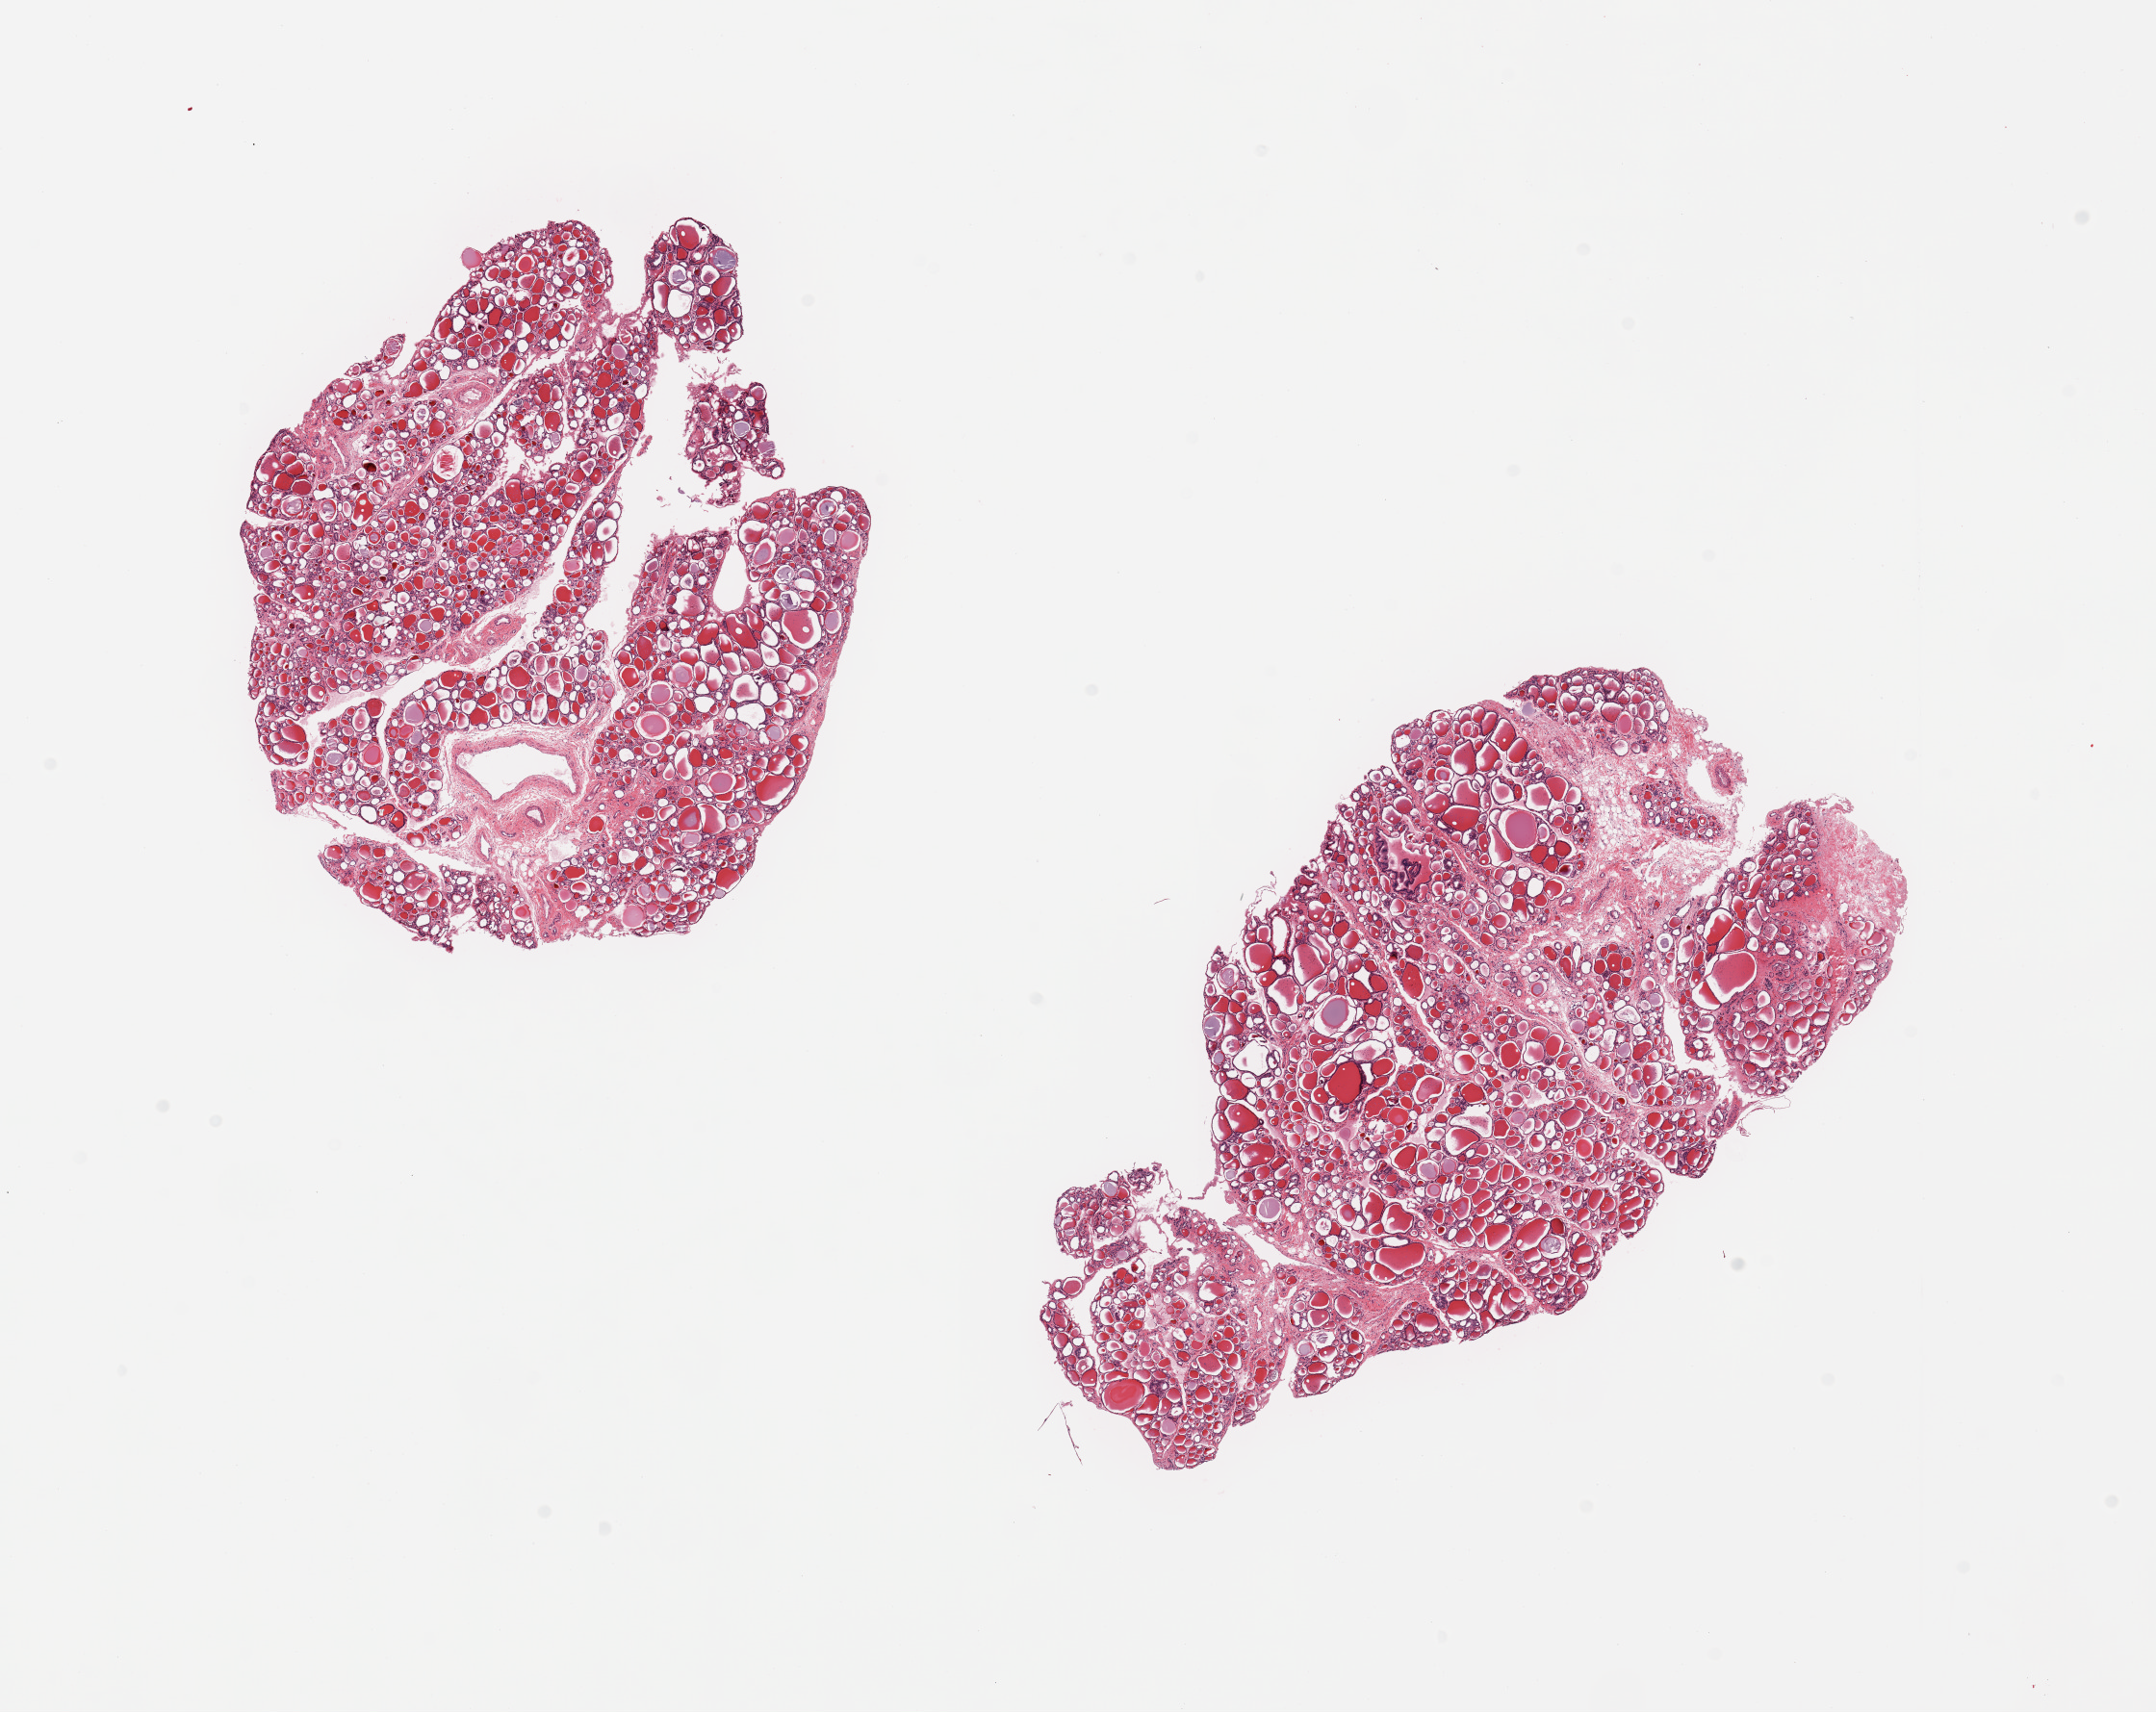
Whole-slide image, hematoxylin and eosin (H&E) stain, low-resolution overview of the scanned area, about 17.7 x 14.1 mm (acquisition: 20x scan); PAXgene-fixed, paraffin-embedded tissue; target tissue: thyroid; donor tissue sample. Donor: female.
Review note (as recorded): 2 pieces.